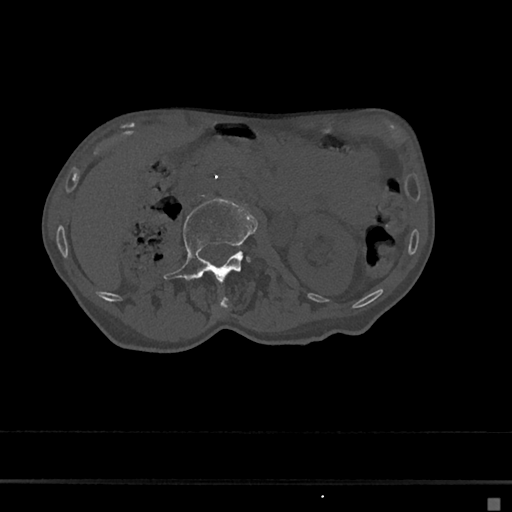
CT including the spine, one axial slice. Slice 15 of 797 in the series (ordered by position). Reconstruction kernel Br40s/3. 120 kVp. Bone window (W 1800 / L 400 HU). 0.5 mm slice thickness. 512 × 512 image matrix, field of view 360 × 360 mm. Patient: female, 68 years. From the clinical record (not read from this slice): primary cancer: renal.
Outlined on this slice (semi-automatic segmentation, software-assisted and operator-edited):
- L1 vertebra: box from (x=217, y=297) to (x=229, y=312) px
- L2 vertebra: (x=163, y=199)–(x=257, y=283)